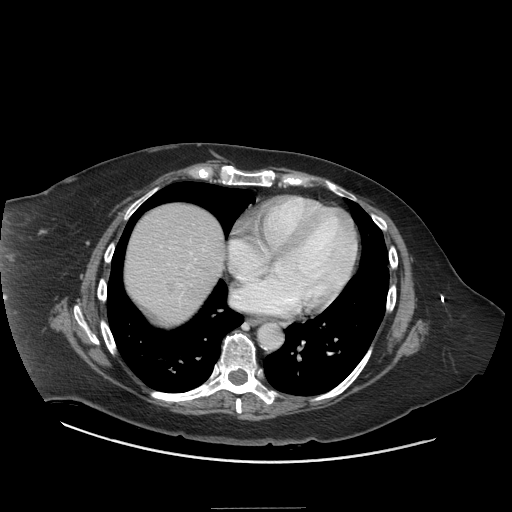
Contrast-enhanced abdominal CT (liver protocol), one axial slice. Slice 70 of 81 in the series (ordered by position). Soft-tissue window (W 400 / L 40 HU). 512 × 512 image matrix, field of view 440 × 440 mm. From the clinical record (not read from this slice): diagnosis: hepatocellular carcinoma (patient treated with transarterial chemoembolisation; whether this scan precedes or follows treatment is not stated here); TNM stage (as recorded): Stage-II; Child-Pugh class: A; tumour differentiation: moderately differentiated; tumour nodularity: multinodular.
Annotated regions visible in this slice (semi-automatic segmentation, software-assisted and operator-edited):
- liver parenchyma outside the tumour (the mass and vessels are separate outlines, so this box may not span the whole liver): box from (x=124, y=204) to (x=224, y=322) px
- liver vessels: (x=146, y=242)–(x=206, y=304)